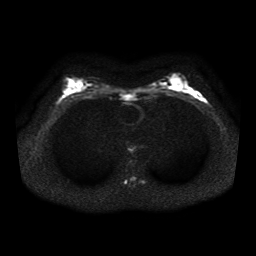
Breast MRI, one axial slice; diffusion-weighted series; image 2 of 4 stored at this slice position (different b-values; order by instance number); 1.5 T; 5 mm slice thickness; 256 × 256 image matrix, field of view 330 × 330 mm. Female patient.
Structures marked on this image (expert manual segmentation):
- tumour on diffusion-weighted imaging: box from (x=192, y=90) to (x=204, y=100) px